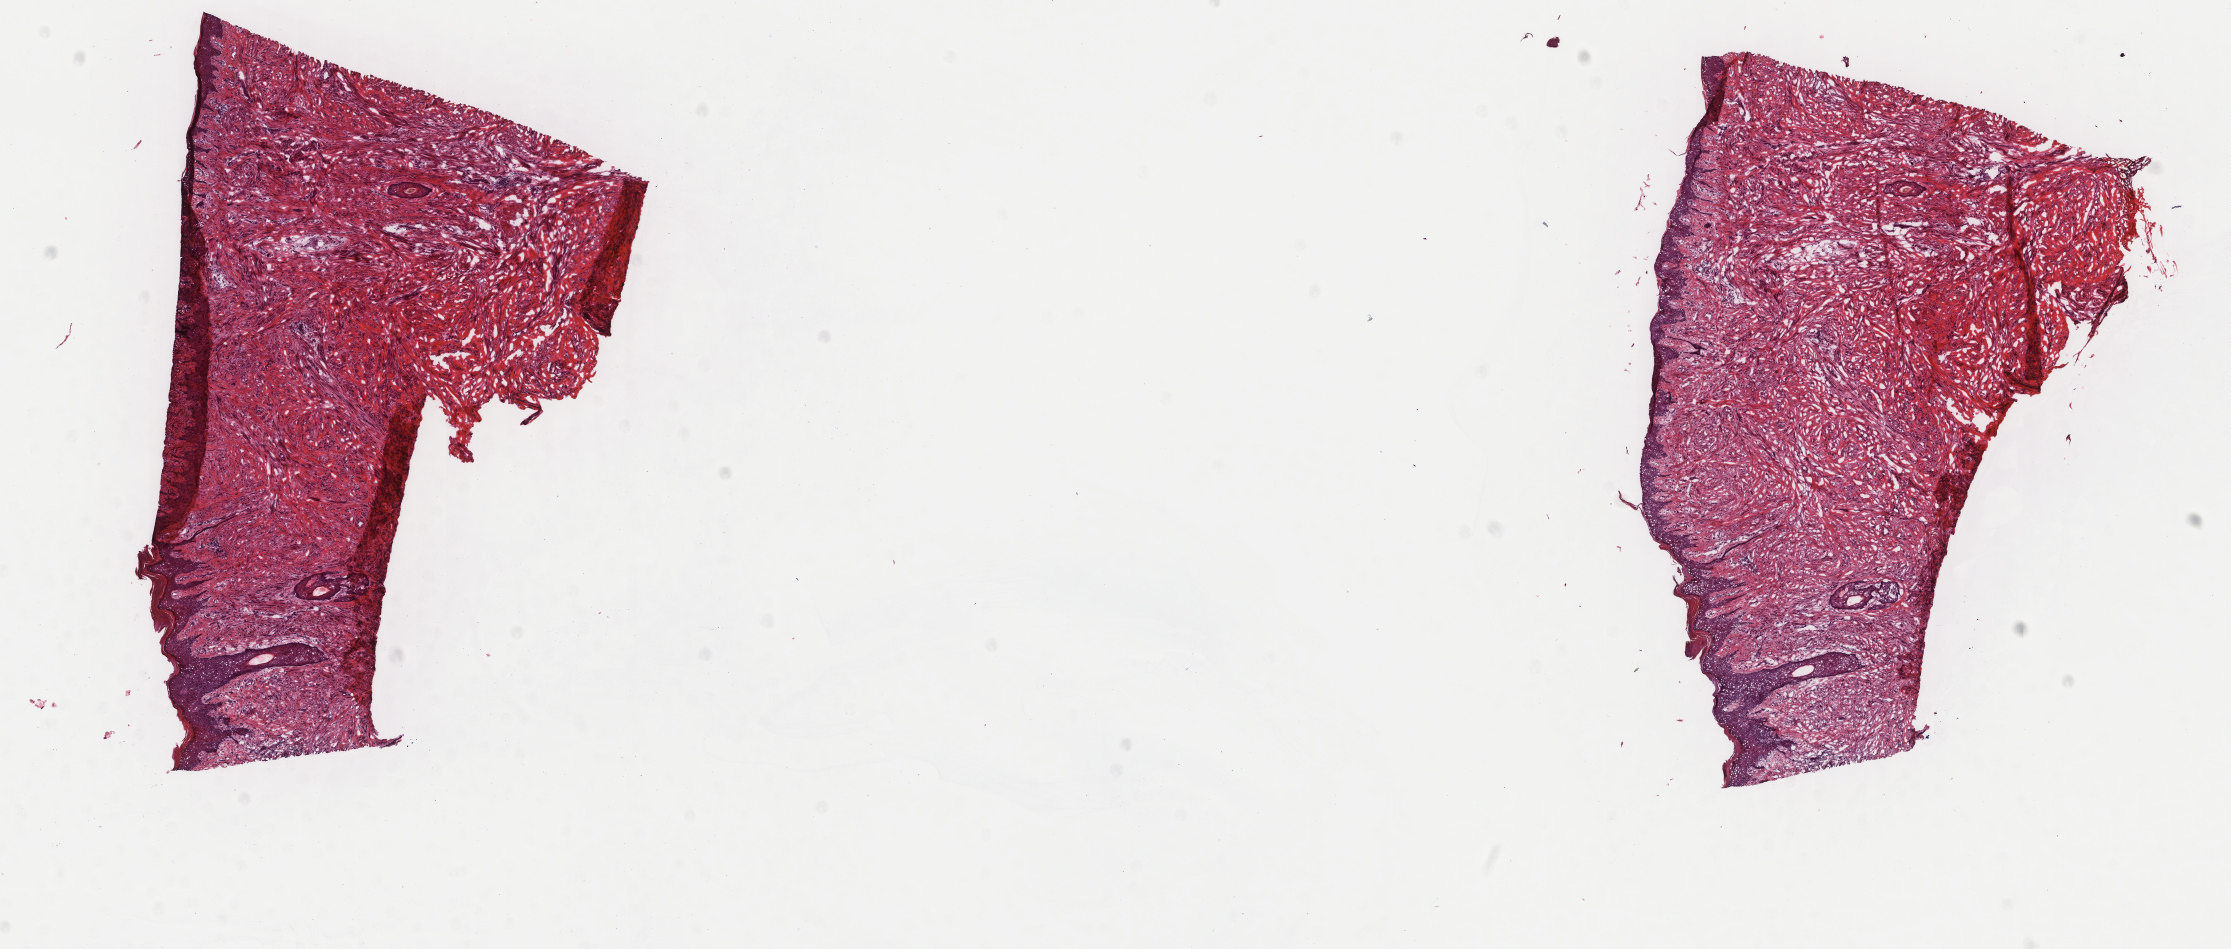
H&E-stained whole-slide image, whole scanned area (about 17.7 x 7.5 mm, from a 40x scan) shown as a low-resolution overview. Frozen section from the top of the tissue portion. Connective, subcutaneous and other soft tissues, primary tumour sample. Male, age 52 years at initial diagnosis.
Histologic diagnosis: Leiomyosarcoma, NOS (connective, subcutaneous and other soft tissues, NOS).